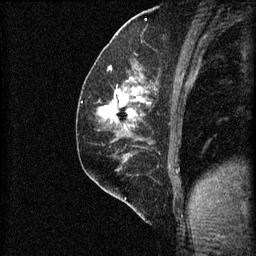
Breast MRI (dynamic contrast-enhanced), one sagittal slice; position 30 of 60 along the scan axis; 3 images stored at this slice position (order not interpretable as contrast timing); 1.5 T; TE 4.2 ms, TR 8.2 ms; 256 × 256 image matrix, field of view 180 × 180 mm. Patient: female, 59 years.
Outlined on this slice (semi-automatically segmented with operator editing):
- analysis volume of interest (the breast-tissue region the enhancement analysis was run in; not a lesion): bounding box (x1, y1, x2, y2) in pixels: (97, 74, 155, 131)
- tumour enhancement mask (voxels above the 70 % enhancement threshold inside the analysis volume of interest): (101, 86, 152, 127)